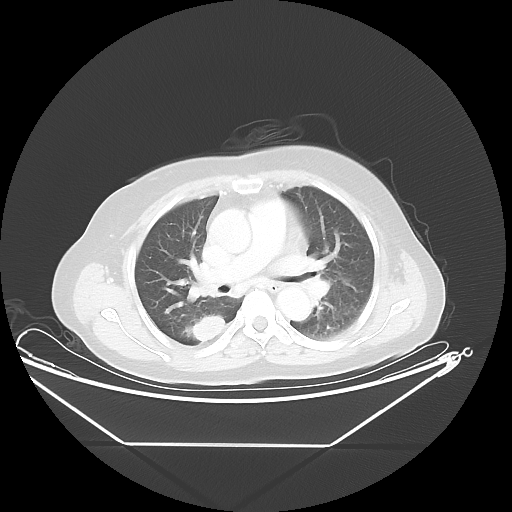
Chest CT, one axial slice; slice 28 of 48 in the series (ordered by position); reconstruction kernel LUNG; 100 kVp; lung window (W 1500 / L -600 HU); 5 mm slice thickness; 512 × 512 image matrix, field of view 462 × 462 mm. Patient: female, 62 years. Case-level facts recorded for this patient, not image findings: clinical TNM (as recorded): T1c N0 M0; histopathological grade: G2-3.
Outlined on this slice (rectangle marked by the reading radiologist):
- lung tumour (recorded histology: adenocarcinoma): bounding box <187,309,237,357> (left, top, right, bottom; pixels)